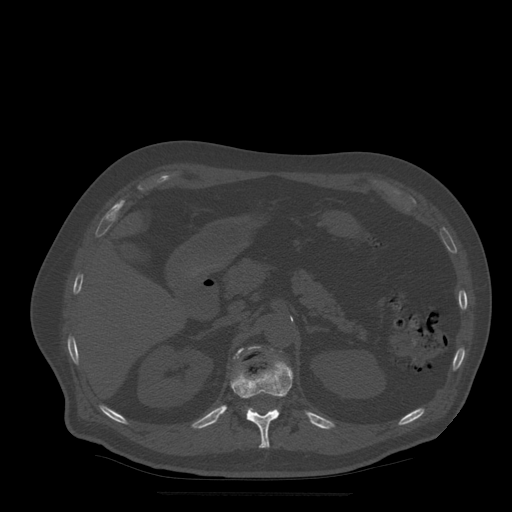
CT including the spine, one axial slice; slice 214 of 522 in the series (ordered by position); bone window (W 1800 / L 400 HU); 1.25 mm slice thickness; 512 × 512 image matrix, field of view 420 × 420 mm. Patient age 72 years. Case-level facts recorded for this patient, not image findings: primary cancer: prostate.
Outlined on this slice (semi-automatic segmentation, software-assisted and operator-edited):
- L1 vertebra: bounding box (x1, y1, x2, y2) in pixels: (236, 347, 260, 416)
- T12 vertebra: (231, 360, 294, 449)